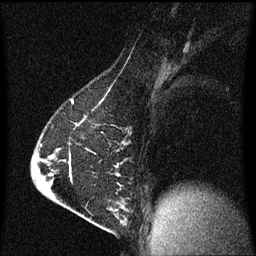
Breast MRI (dynamic contrast-enhanced), one sagittal slice. Slice 39 of 60 in the series (ordered by position). Dynamic contrast-enhanced series, image 2 of 3 at this slice position (ordered by acquisition). 1.5 T. TE 4.2 ms, TR 8 ms. 256 × 256 image matrix, field of view 200 × 200 mm. Female patient, age 63 years.
Structures marked on this image (semi-automatic segmentation, software-assisted and operator-edited):
- analysis volume of interest (the breast-tissue region the enhancement analysis was run in; not a lesion): box from (x=88, y=184) to (x=129, y=229) px
- tumour enhancement mask (voxels above the 70 % enhancement threshold inside the analysis volume of interest): (x=118, y=184)–(x=123, y=223)